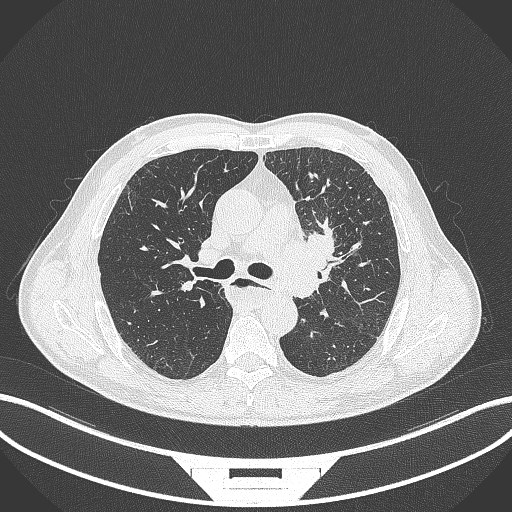
Chest CT, one axial slice. Position 237 of 411 along the scan axis. Reconstruction kernel B70f. 120 kVp. Lung window (W 1500 / L -600 HU). 512 × 512 image matrix, field of view 400 × 400 mm. Patient: male, 57 years. Case-level facts recorded for this patient, not image findings: clinical TNM (as recorded): T2a N1 M0.
Outlined on this slice (rectangle marked by the reading radiologist):
- lung tumour (recorded histology: squamous cell carcinoma): bounding box (x1, y1, x2, y2) in pixels: (273, 224, 351, 309)